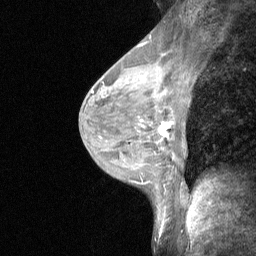
Breast MRI (dynamic contrast-enhanced), one sagittal slice. Position 35 of 64 along the scan axis. Dynamic contrast-enhanced study with each time point stored as its own series, time point 2 of 3 at this slice position (early post-contrast, ordered by acquisition time). 1.5 T. TE 4.8 ms, TR 27 ms. 2 mm slice thickness. 256 × 256 image matrix. Female patient, age 44 years. Case-level facts recorded for this patient, not image findings: setting: breast cancer imaged before/during neoadjuvant chemotherapy; receptor status: HR-positive, HER2-negative.
Annotated regions visible in this slice (semi-automatic segmentation, software-assisted and operator-edited):
- analysis volume of interest (the breast-tissue region the enhancement analysis was run in; not a lesion): box from (x=140, y=109) to (x=180, y=148) px
- tumour enhancement mask (voxels above the 90 % enhancement threshold inside the analysis volume of interest): (x=159, y=122)–(x=173, y=136)